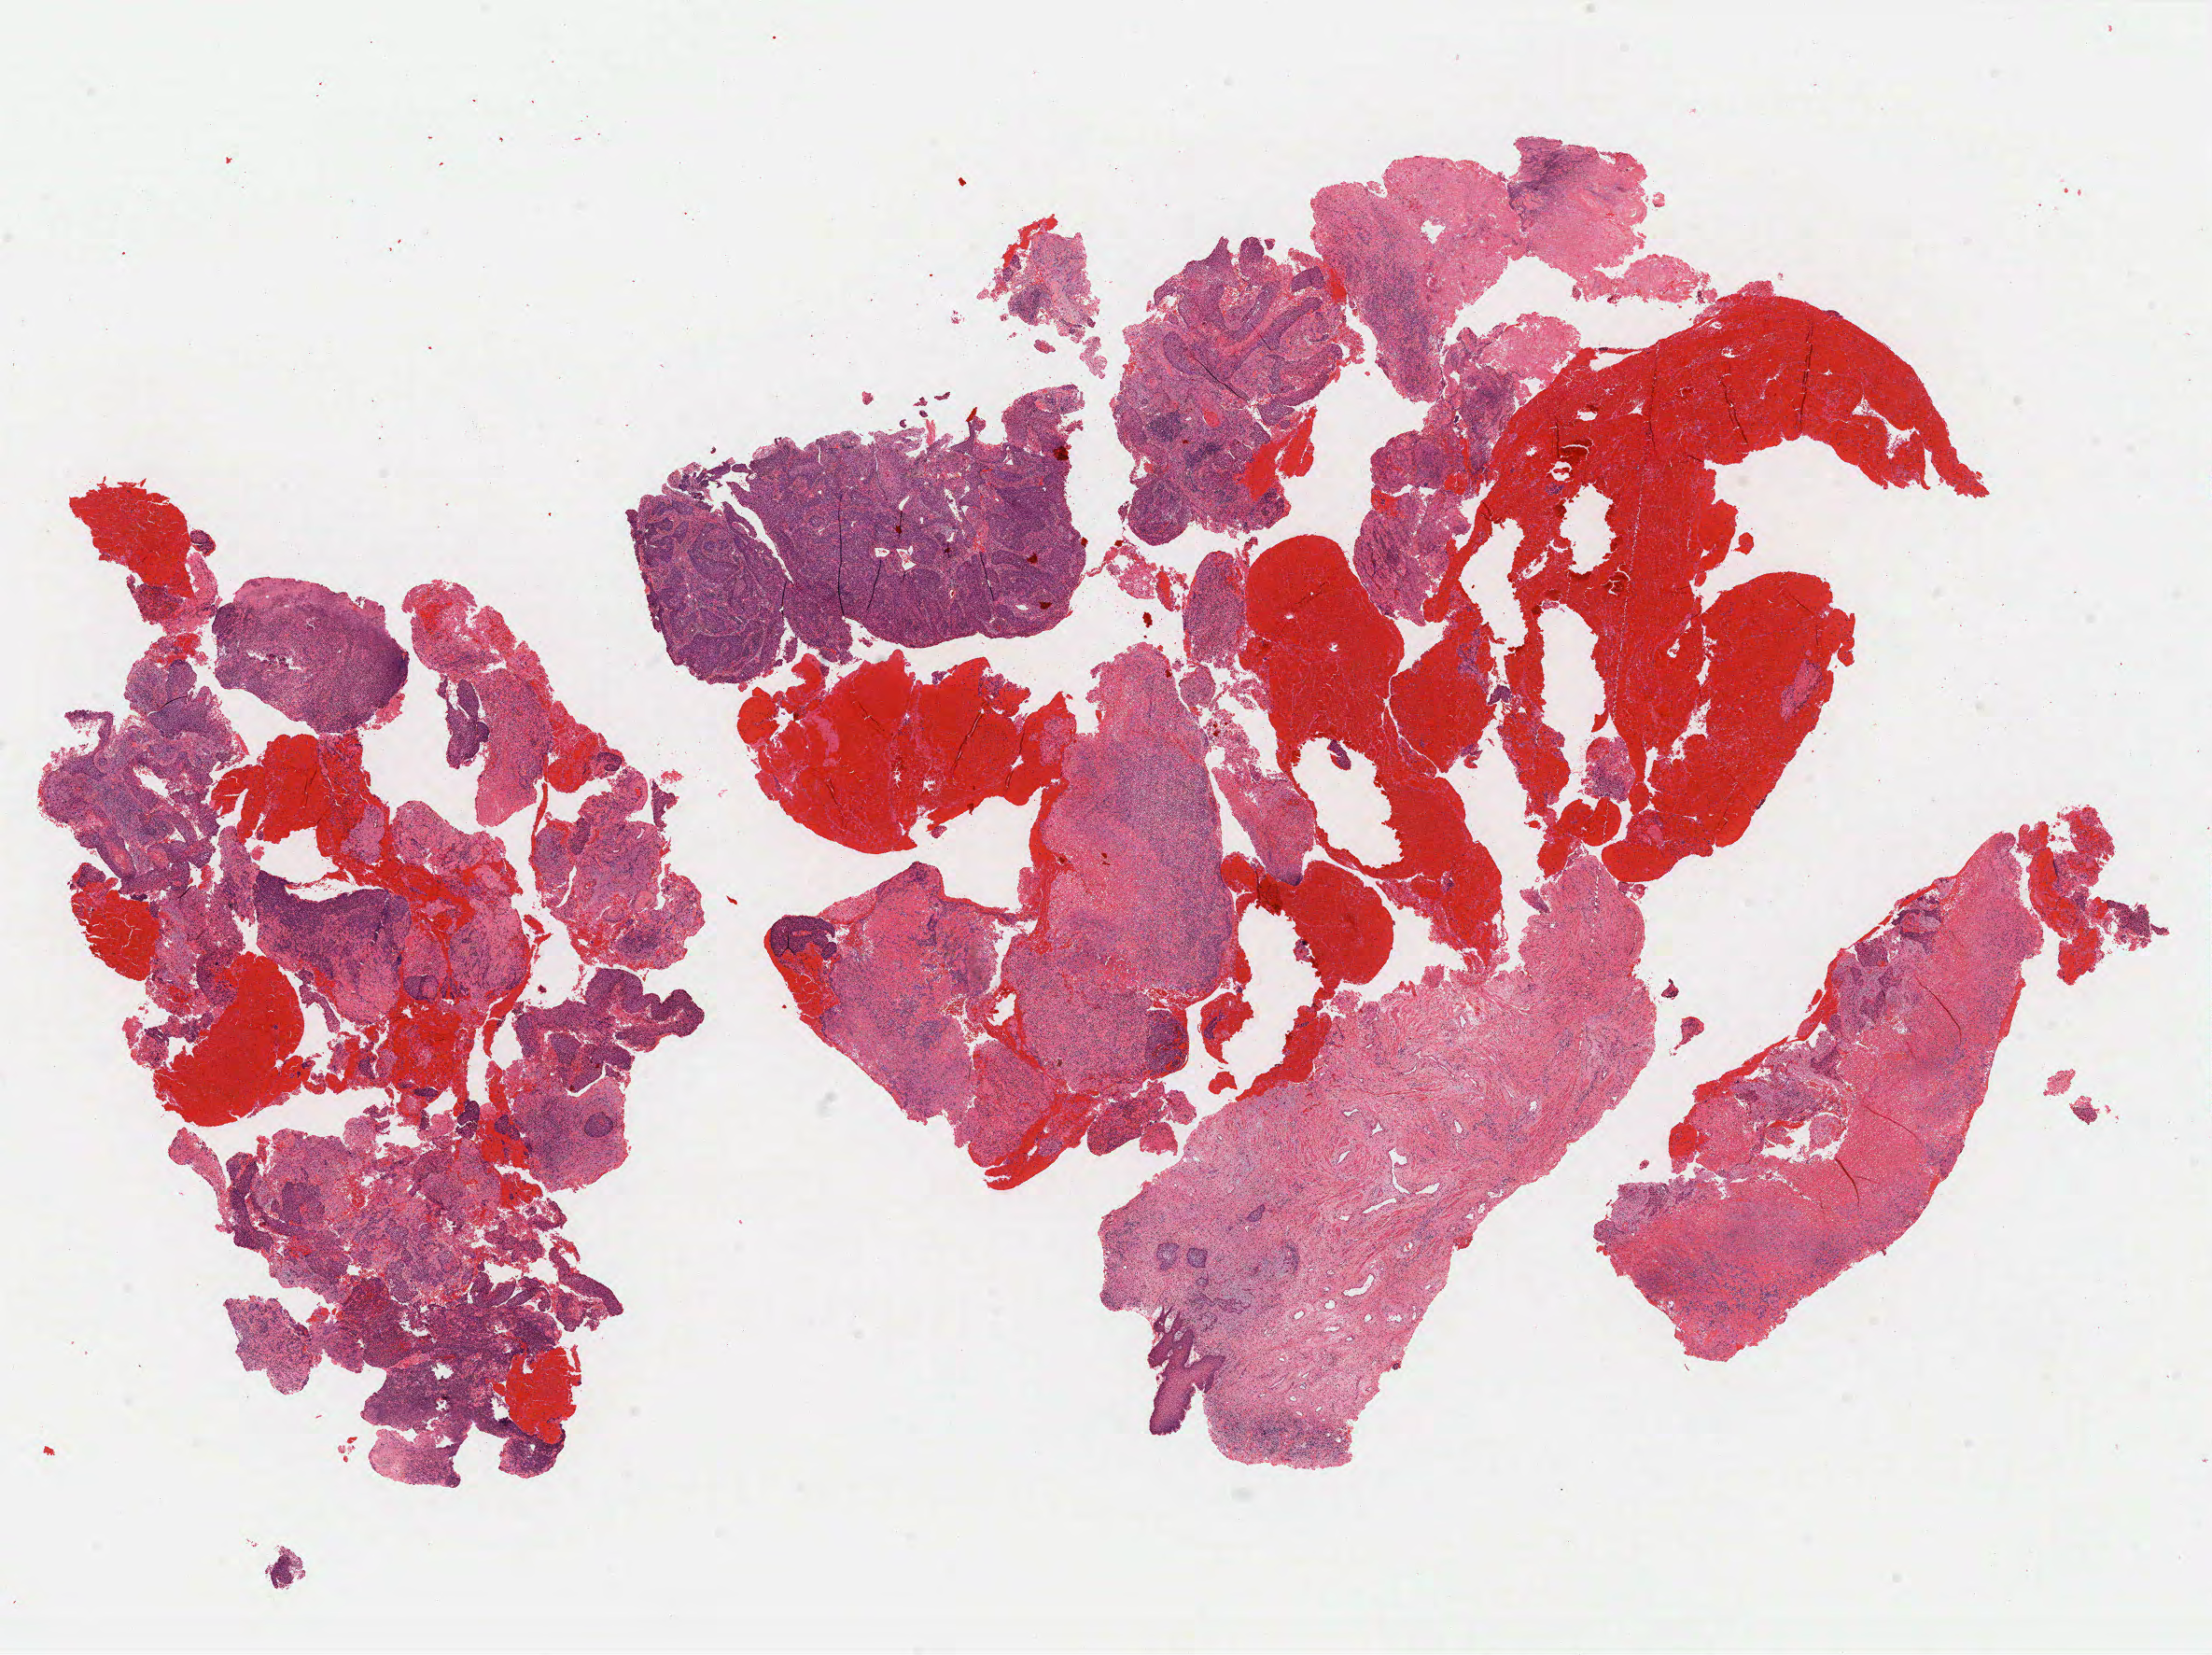
Digitized Hematoxylin and eosin (H&E) stained tissue section (whole slide), shown as a low-resolution overview of the whole scanned area (about 19.0 x 14.2 mm), formalin-fixed paraffin-embedded (FFPE) diagnostic section, sample: primary tumour, cervix. Female, age 58 years at initial diagnosis. Histologic grade: G2 (moderately differentiated).
Histologic diagnosis: Squamous cell carcinoma, NOS (cervix uteri). FIGO stage: IVA.